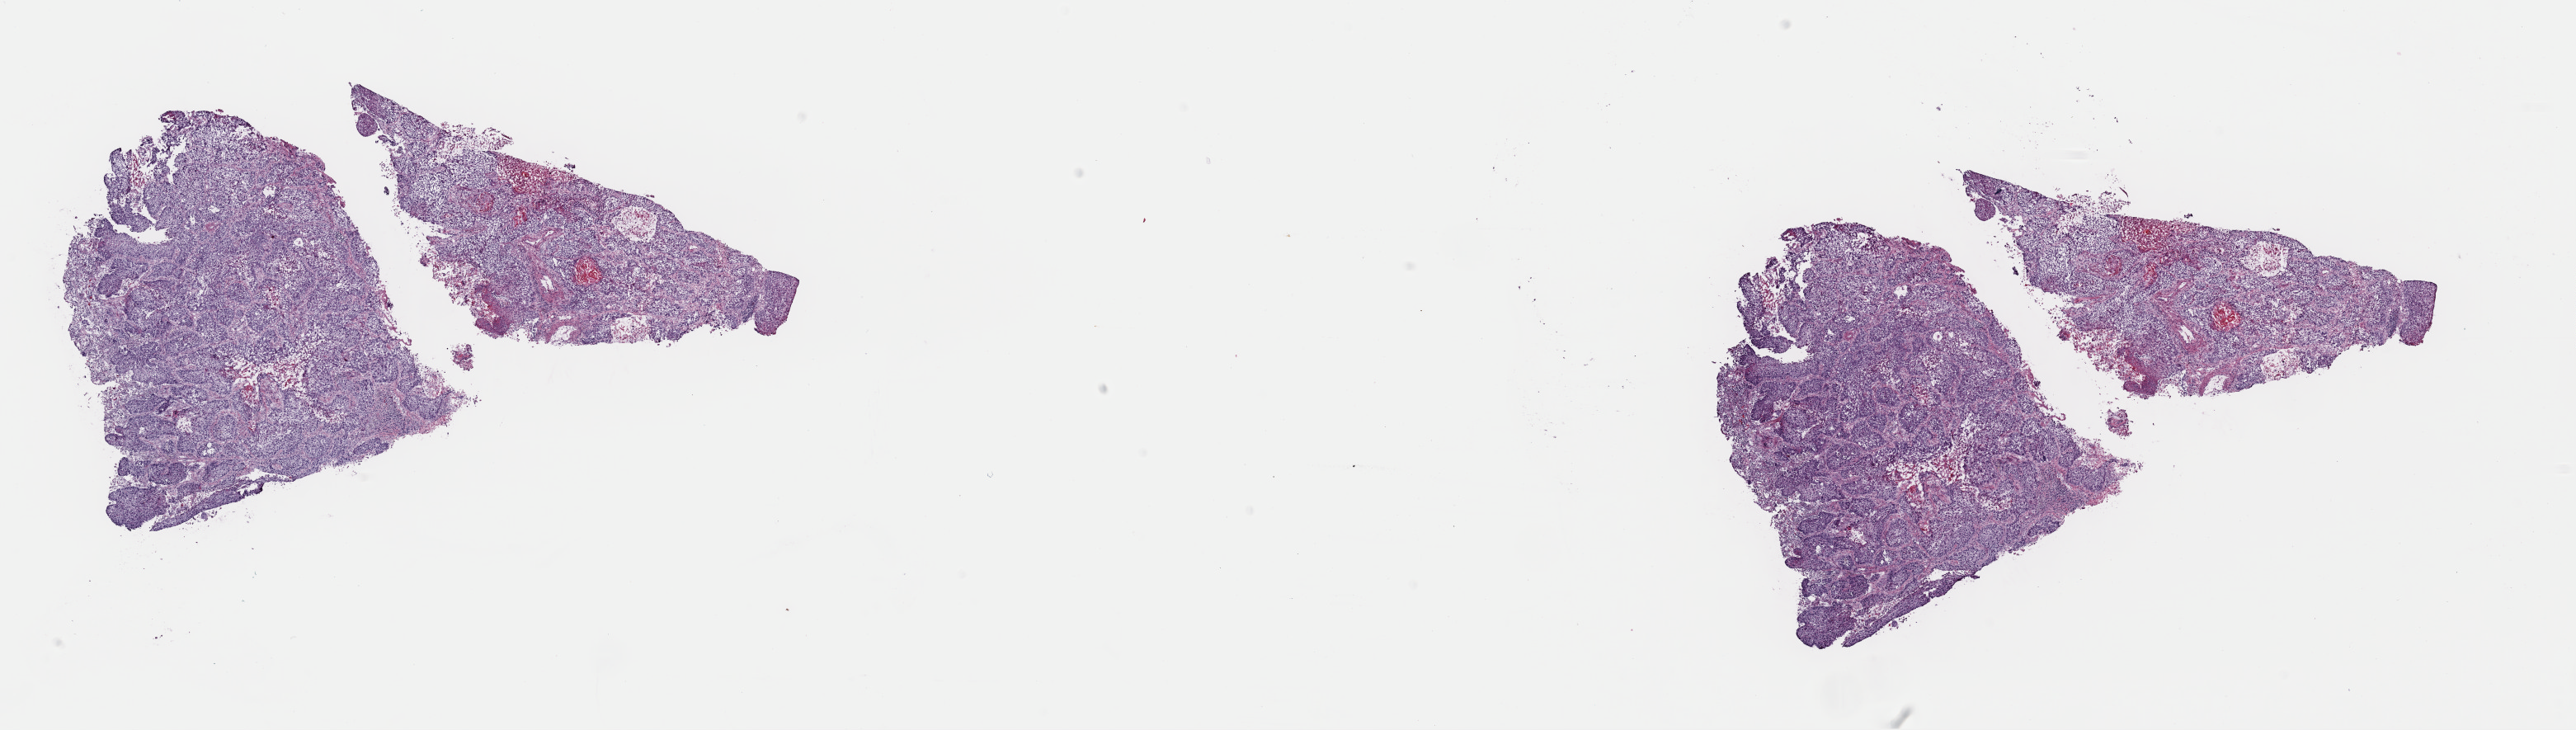
Whole-slide histology image, H&E-stained, a low-resolution overview of the entire scanned area, about 24.7 x 7.0 mm (slide scanned at 40x), frozen section from the top of the tissue portion, primary tumour sample from the lung. Patient: male, age at initial diagnosis 68 years. Composition of this section per pathologist review: tumour cells 75%, tumour nuclei 100%, normal cells 0%, stromal cells 23%, necrosis 2%. Inflammatory infiltration, as recorded: lymphocyte infiltration 2%, monocyte infiltration 6%, neutrophil infiltration 2%.
* AJCC pathologic stage: IA (7th edition)
* pathologic diagnosis: Squamous cell carcinoma, NOS